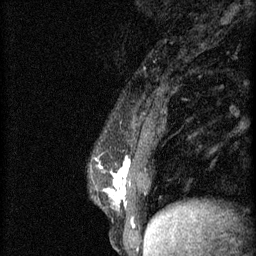
Breast MRI (dynamic contrast-enhanced), one sagittal slice; slice 17 of 60 in the series (ordered by position); 3 images stored at this slice position (order not interpretable as contrast timing); 1.5 T; TE 4.2 ms, TR 11 ms; 2 mm slice thickness; 256 × 256 image matrix, field of view 180 × 180 mm. Patient: female, 37 years.
Structures marked on this image (semi-automatic segmentation, software-assisted and operator-edited):
- analysis volume of interest (the breast-tissue region the enhancement analysis was run in; not a lesion): bounding box [x1, y1, x2, y2] px = [94, 146, 174, 221]
- tumour enhancement mask (voxels above the 70 % enhancement threshold inside the analysis volume of interest): [100, 158, 130, 203]